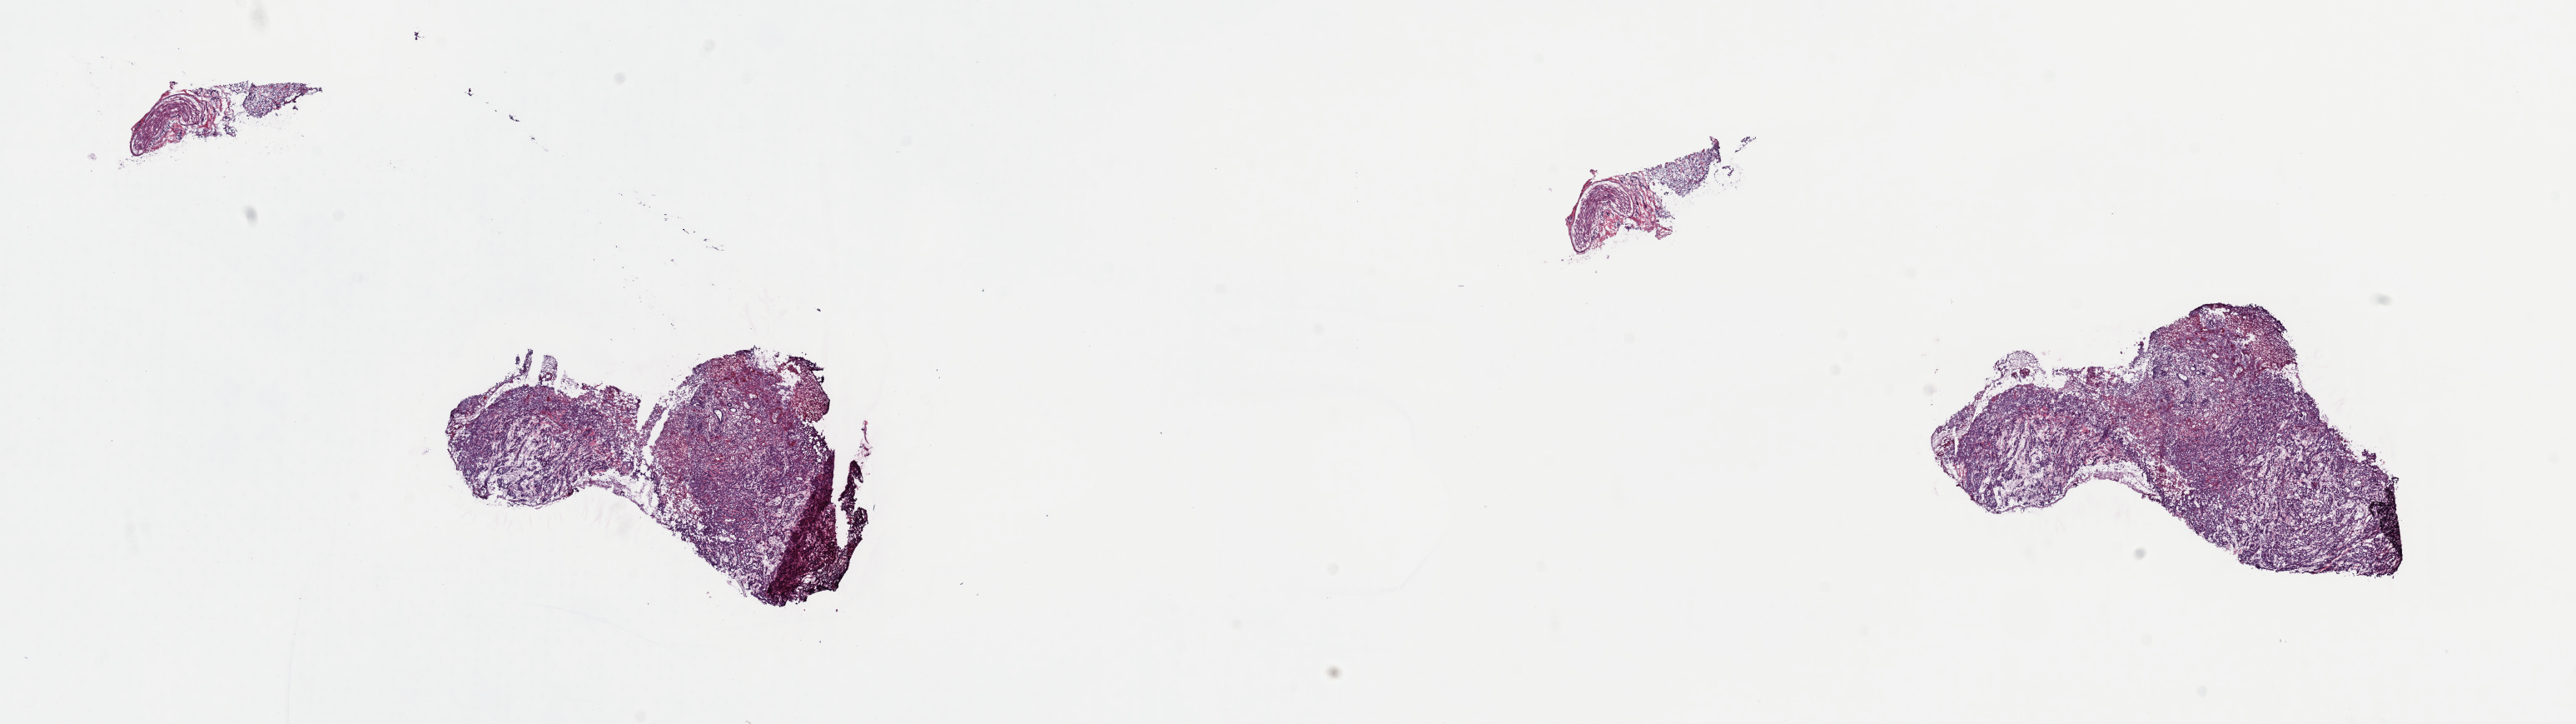
Digitized Hematoxylin and eosin (H&E) stained tissue section (whole slide), whole scanned area (about 24.4 x 6.9 mm, acquisition: 40x scan) shown as a low-resolution overview, frozen section, primary tumour sample from the head and neck. Male patient; age at initial diagnosis 59 years. Histologic grade: G2 (moderately differentiated). Pathologist review of this section (percent, as recorded): tumour cells 70%, tumour nuclei 80%, normal cells 10%, stromal cells 10%, necrosis 10%. Inflammatory infiltration, as recorded: lymphocyte infiltration 0%, monocyte infiltration 0%, neutrophil infiltration 0%.
- AJCC pathologic stage: III (7th edition)
- diagnosis: Squamous cell carcinoma, keratinizing, NOS (floor of mouth, NOS)